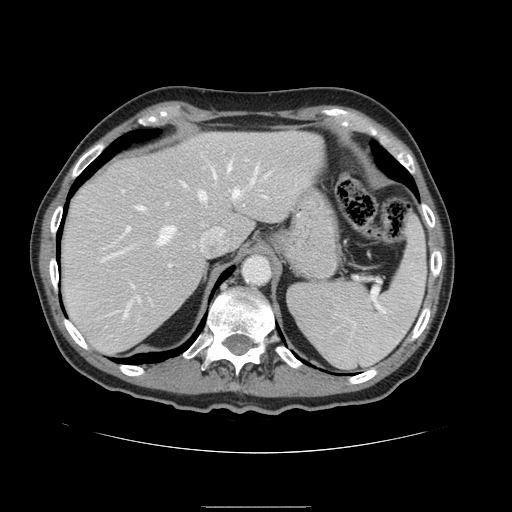
Contrast-enhanced abdominal CT, one axial slice; slice 116 of 168 in the series (ordered by position); soft-tissue window (W 400 / L 40 HU); 2.5 mm slice thickness; 512 × 512 image matrix, field of view 386 × 386 mm. Male patient, age 74 years. Case-level facts recorded for this patient, not image findings: diagnosis: colorectal cancer liver metastases, imaged before liver resection; multiple liver metastases: no.
Structures marked on this image (outlined manually by an expert reader):
- hepatic veins: box from (x=102, y=162) to (x=272, y=303) px
- liver: (x=61, y=131)–(x=324, y=355)
- planned liver remnant (the part of the liver to remain after resection): (x=61, y=131)–(x=325, y=355)
- portal vein (with intrahepatic branches): (x=121, y=195)–(x=267, y=288)